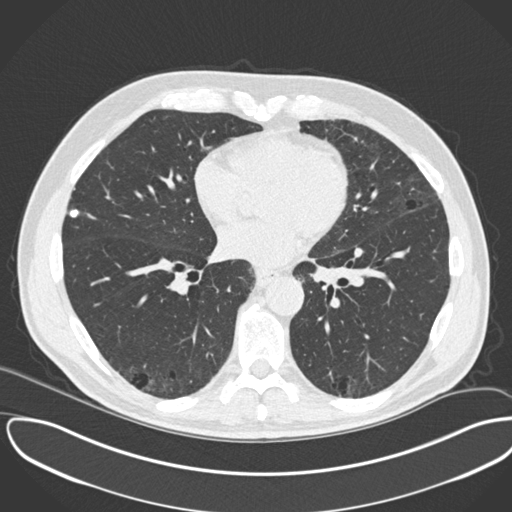
Low-dose screening chest CT, one axial slice. Position 109 of 245 along the scan axis. Reconstruction kernel B30f. Lung window (W 1500 / L -600 HU). 2 mm slice thickness. 512 × 512 image matrix, field of view 396 × 396 mm.
Annotated regions visible in this slice (expert manual segmentation):
- lesion 1 (tumor, upper lobe of right lung): box from (x=69, y=208) to (x=80, y=219) px